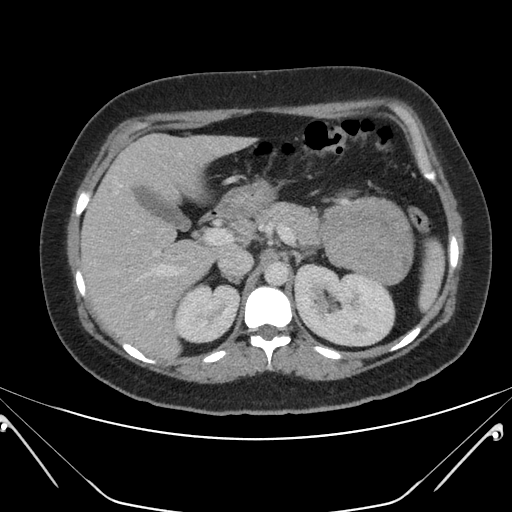
Contrast-enhanced abdominal CT, one axial slice. Slice 128 of 168 in the series (ordered by position). Soft-tissue window (W 400 / L 40 HU). 512 × 512 image matrix, field of view 394 × 394 mm. Female patient, age 26 years. From the clinical record (not read from this slice): diagnosis: adrenocortical carcinoma; tumour side: left adrenal; tumour size at pathology: 28 cm; Ki-67 index: 20 %; stage (as recorded): 2.
Outlined on this slice (semi-automatic segmentation, software-assisted and operator-edited):
- mass: bounding box [x1, y1, x2, y2] px = [323, 198, 412, 282]